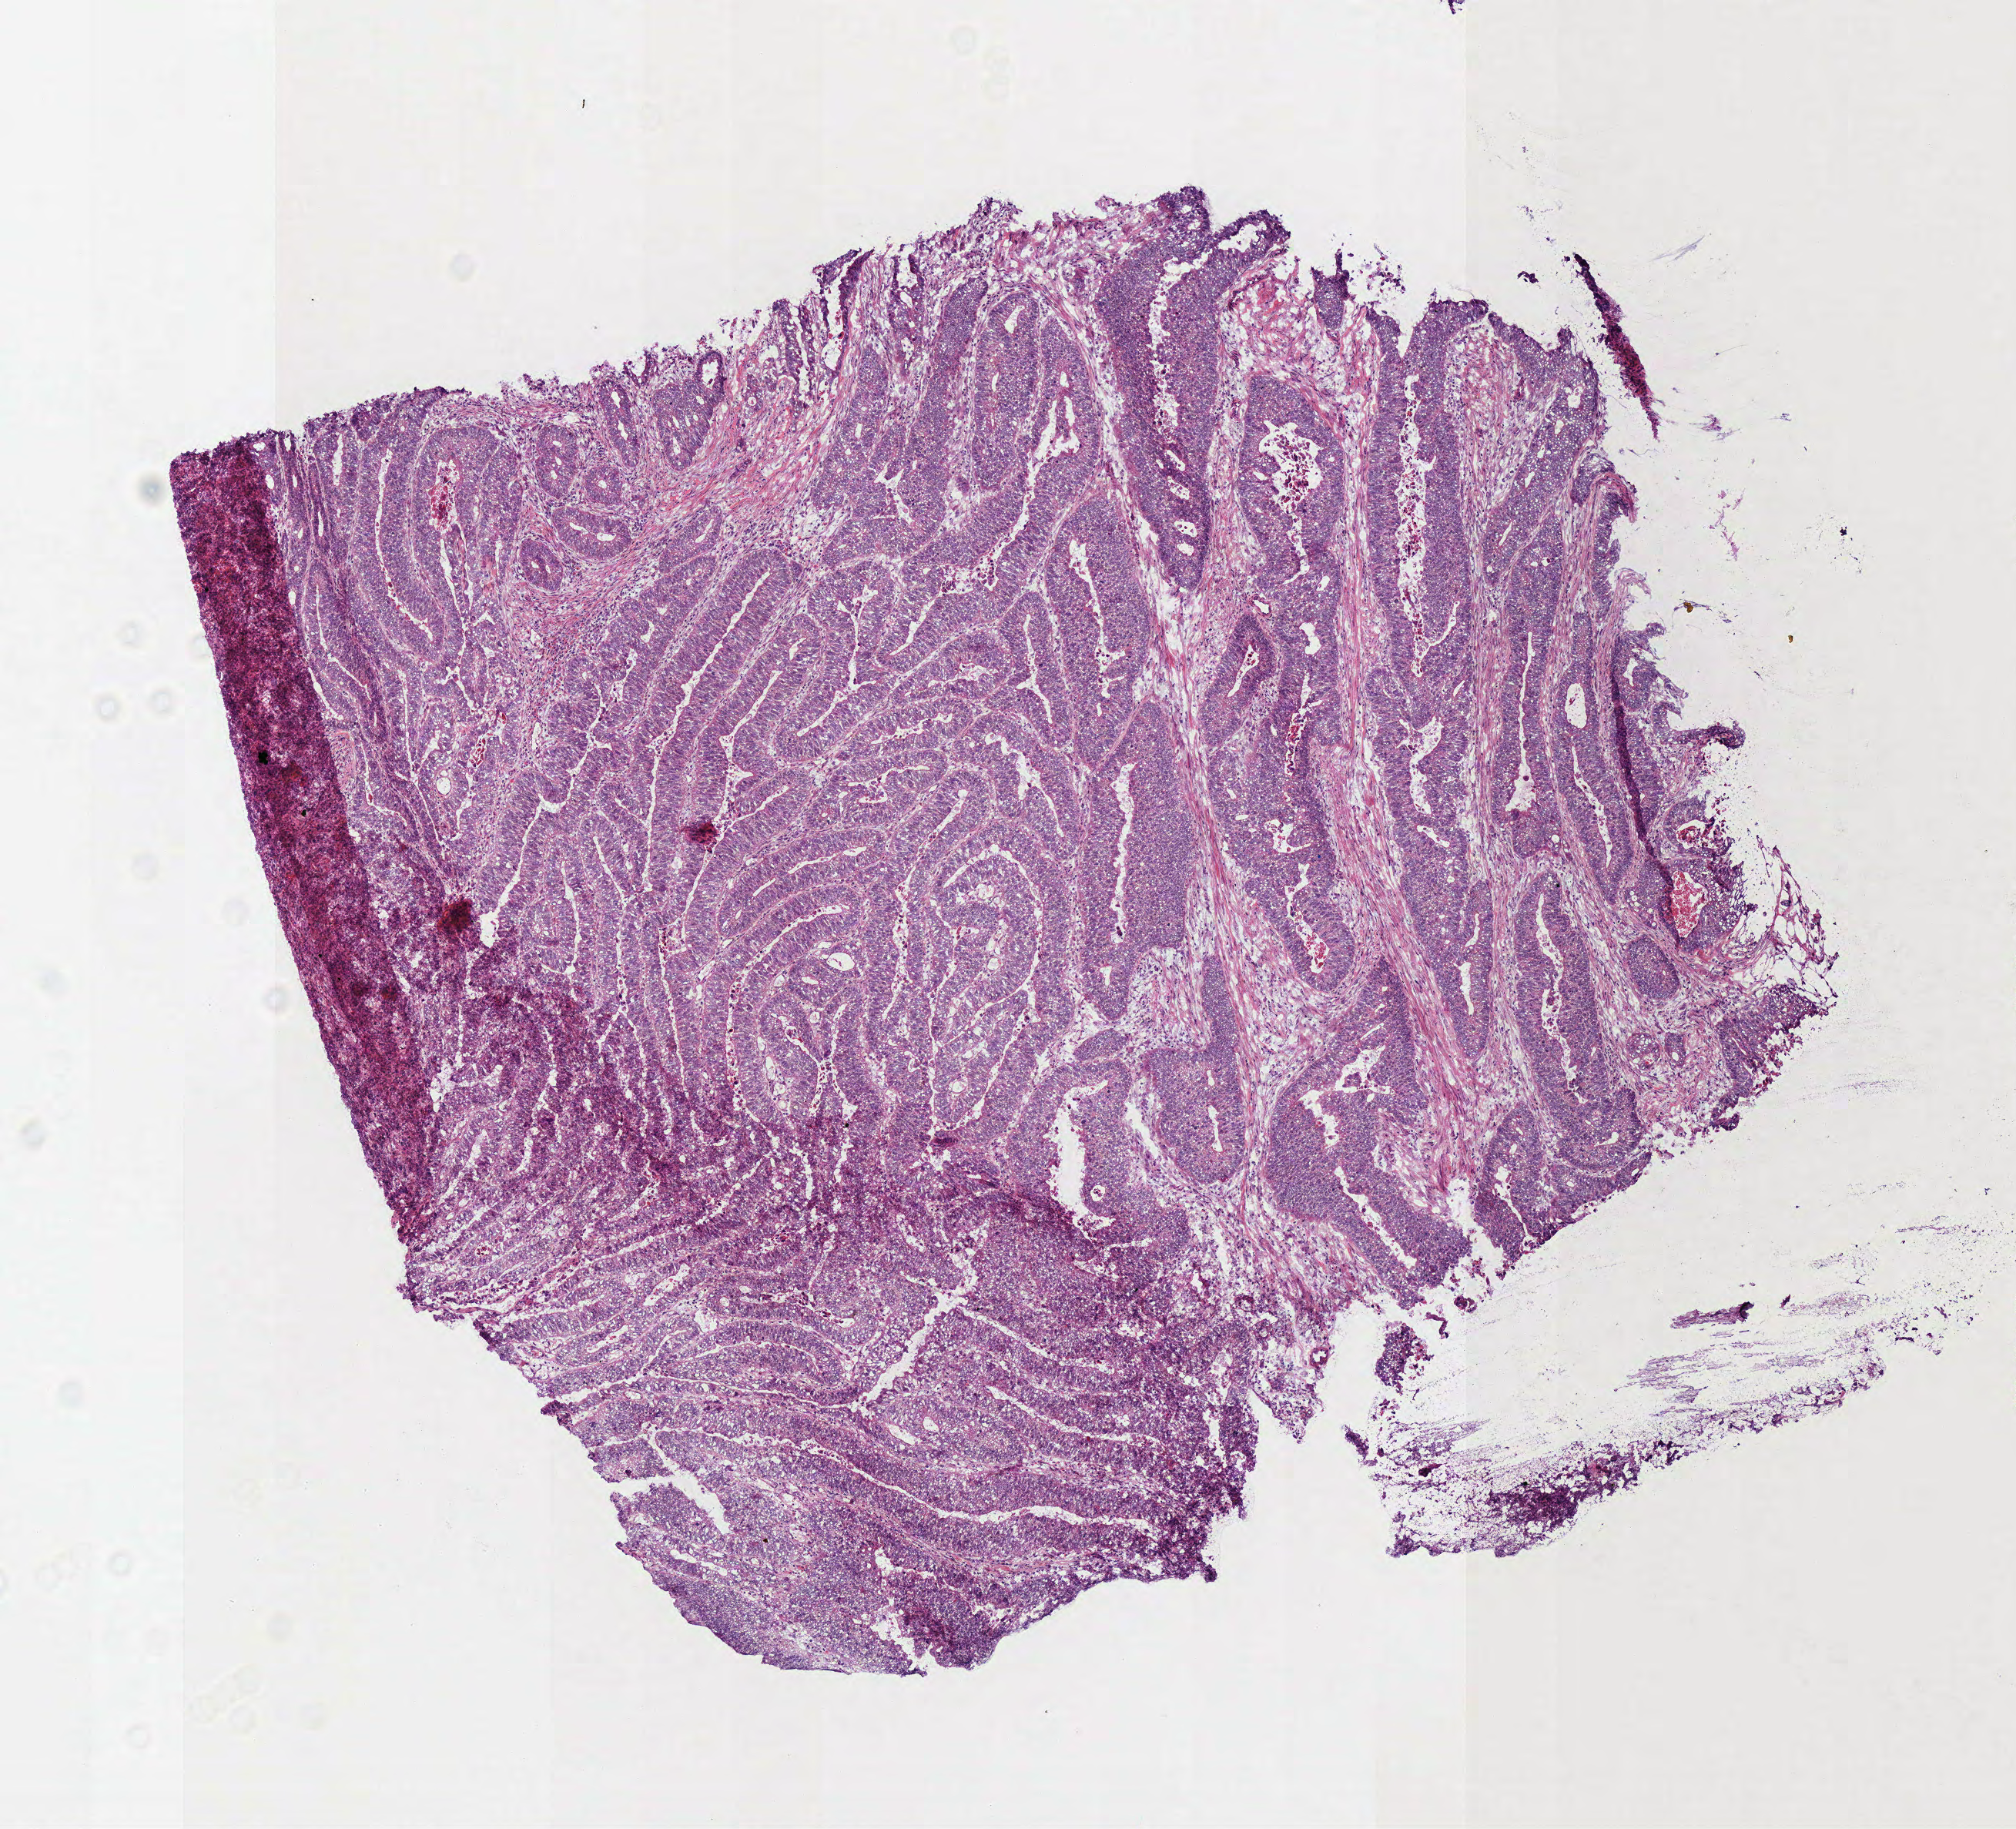
Whole-slide histology image, Hematoxylin and eosin (H&E) stained, whole scanned area (about 5.2 x 4.7 mm, acquisition: 40x scan) shown as a low-resolution overview; frozen section from the bottom of the tissue portion; sample: primary tumour, rectum. Male, age 60 years at initial diagnosis. Pathologist review of this section (percent, as recorded): tumour cells 87%, tumour nuclei 85%, normal cells 0%, stromal cells 10%, necrosis 3%.
* pathologic diagnosis: Adenocarcinoma in tubulovillous adenoma
* TNM: T3 N1 M0
* AJCC pathologic stage: IIIA (6th edition)
* lymph nodes positive (case pathology): 1 of 18 examined